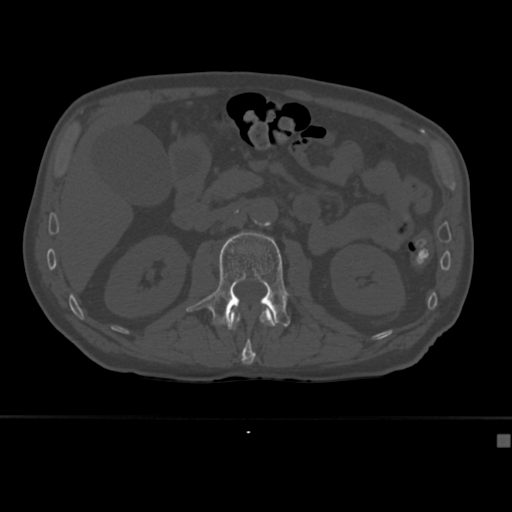
CT including the spine, one axial slice; slice 154 of 430 in the series (ordered by position); reconstruction kernel Br40s; 120 kVp; bone window (W 1800 / L 400 HU); 512 × 512 image matrix, field of view 337 × 337 mm. Male patient, age 64 years. From the clinical record (not read from this slice): primary cancer: uterus; vertebrae with lytic lesions (as recorded): T1, T4, T5, T7, L5.
Outlined on this slice (semi-automatic segmentation, software-assisted and operator-edited):
- L1 vertebra: bounding box [x1, y1, x2, y2] px = [228, 308, 276, 365]
- L2 vertebra: [186, 232, 290, 327]